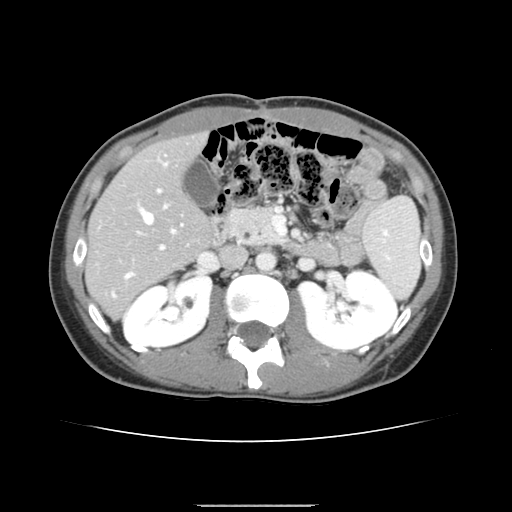
Contrast-enhanced abdominal CT, one axial slice. Slice 75 of 150 in the series (ordered by position). 120 kVp. Soft-tissue window (W 400 / L 40 HU). 2.5 mm slice thickness. 512 × 512 image matrix, field of view 324 × 324 mm. Female patient, age 32 years. From the clinical record (not read from this slice): diagnosis: colorectal cancer liver metastases, imaged before liver resection; multiple liver metastases: yes; largest metastasis: 0.7 cm.
Outlined on this slice (outlined manually by an expert reader):
- hepatic veins: bounding box [x1, y1, x2, y2] px = [126, 209, 175, 278]
- liver: [86, 134, 211, 317]
- planned liver remnant (the part of the liver to remain after resection): [87, 135, 211, 281]
- portal vein (with intrahepatic branches): [112, 162, 183, 296]